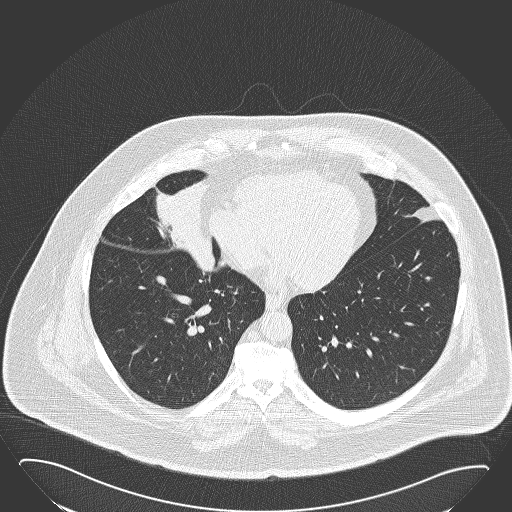
Low-dose screening chest CT, one axial slice. Position 64 of 168 along the scan axis. 120 kVp. Lung window (W 1500 / L -600 HU). 2 mm slice thickness. 512 × 512 image matrix, field of view 432 × 432 mm.
Structures marked on this image (manually delineated by an expert):
- lesion 1 (tumor, hilum of right lung): box from (x=156, y=178) to (x=215, y=273) px